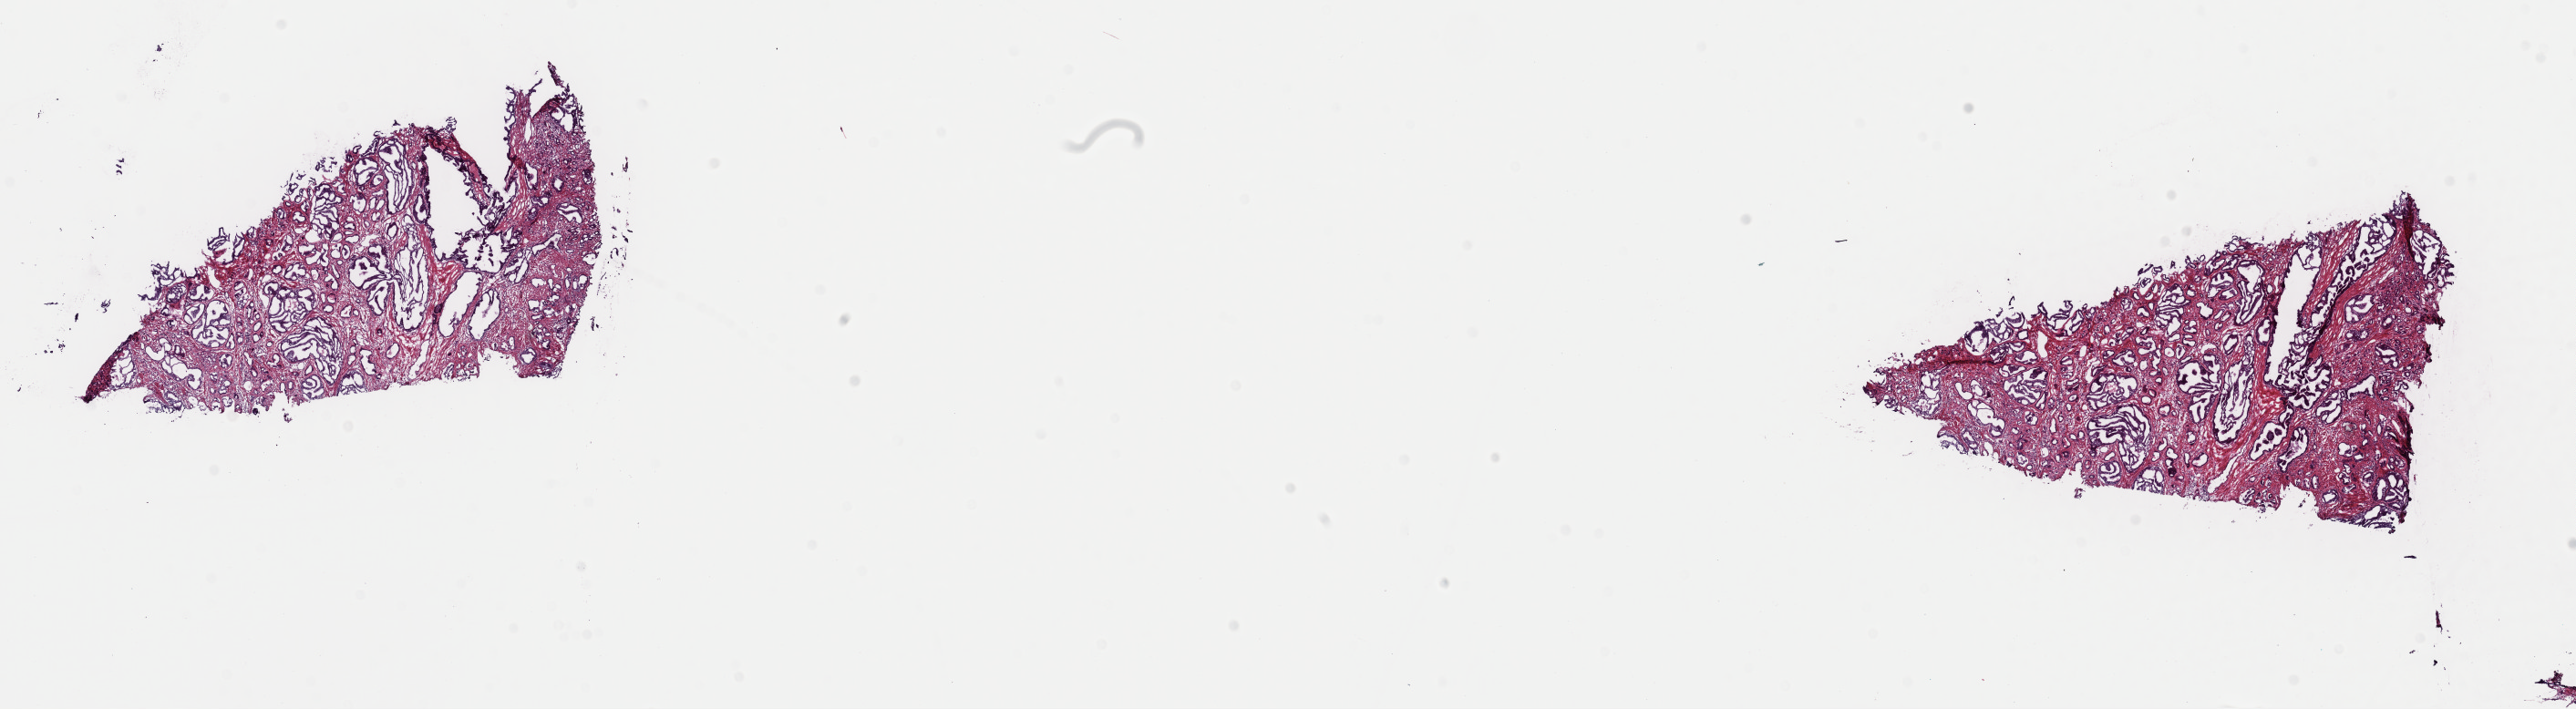
Digitized Hematoxylin and eosin (H&E) stained tissue section (whole slide) — a low-resolution overview of the entire scanned area, about 22.3 x 6.1 mm (acquisition: 40x scan); frozen section; primary tumour sample from the prostate. Male, age 56 years at initial diagnosis. Gleason score: 9 (4+5). Composition of this section per pathologist review: tumour cells 70%, tumour nuclei 80%, normal cells 0%, stromal cells 30%, necrosis 0%. Infiltration values recorded for this section: lymphocyte infiltration 0%, monocyte infiltration 0%, neutrophil infiltration 0%.
Laterality: bilateral. Diagnosis: Adenocarcinoma, NOS (prostate gland). Lymph nodes positive (case pathology): 2 of 4 examined.